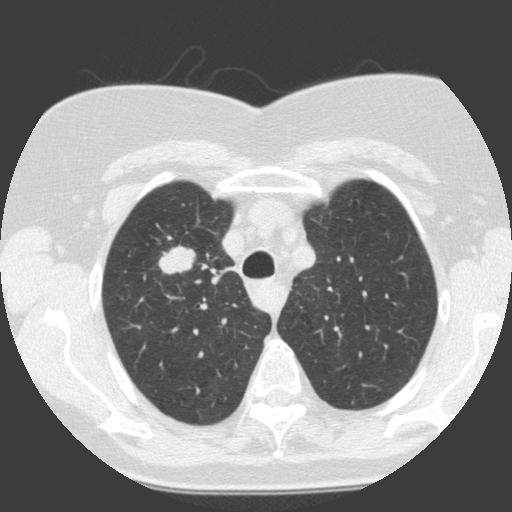
Axial slice from a low-dose chest CT screening exam. First (baseline) screen. Lung window (W 1500 / L -600 HU). Standard (soft-tissue) reconstruction kernel (C). Slice 33 of 146 in the series. Female participant, aged 68 years at enrolment. Current smoker at enrolment.
Lesion marked by an expert reader, bounding box <155,240,203,285> (left, top, right, bottom; pixels). The exam's reader record, not a measurement of the box and not confirmed to be the same lesion: non-calcified nodule or mass ≥4 mm, right upper lobe, 19 × 12 mm, smooth margins, soft tissue attenuation. Later outcome: lung cancer diagnosed 30 days after this screen — squamous cell carcinoma, NOS, right upper lobe, moderately differentiated (G2), stage IA (AJCC 6th edition), 28 mm at pathology.